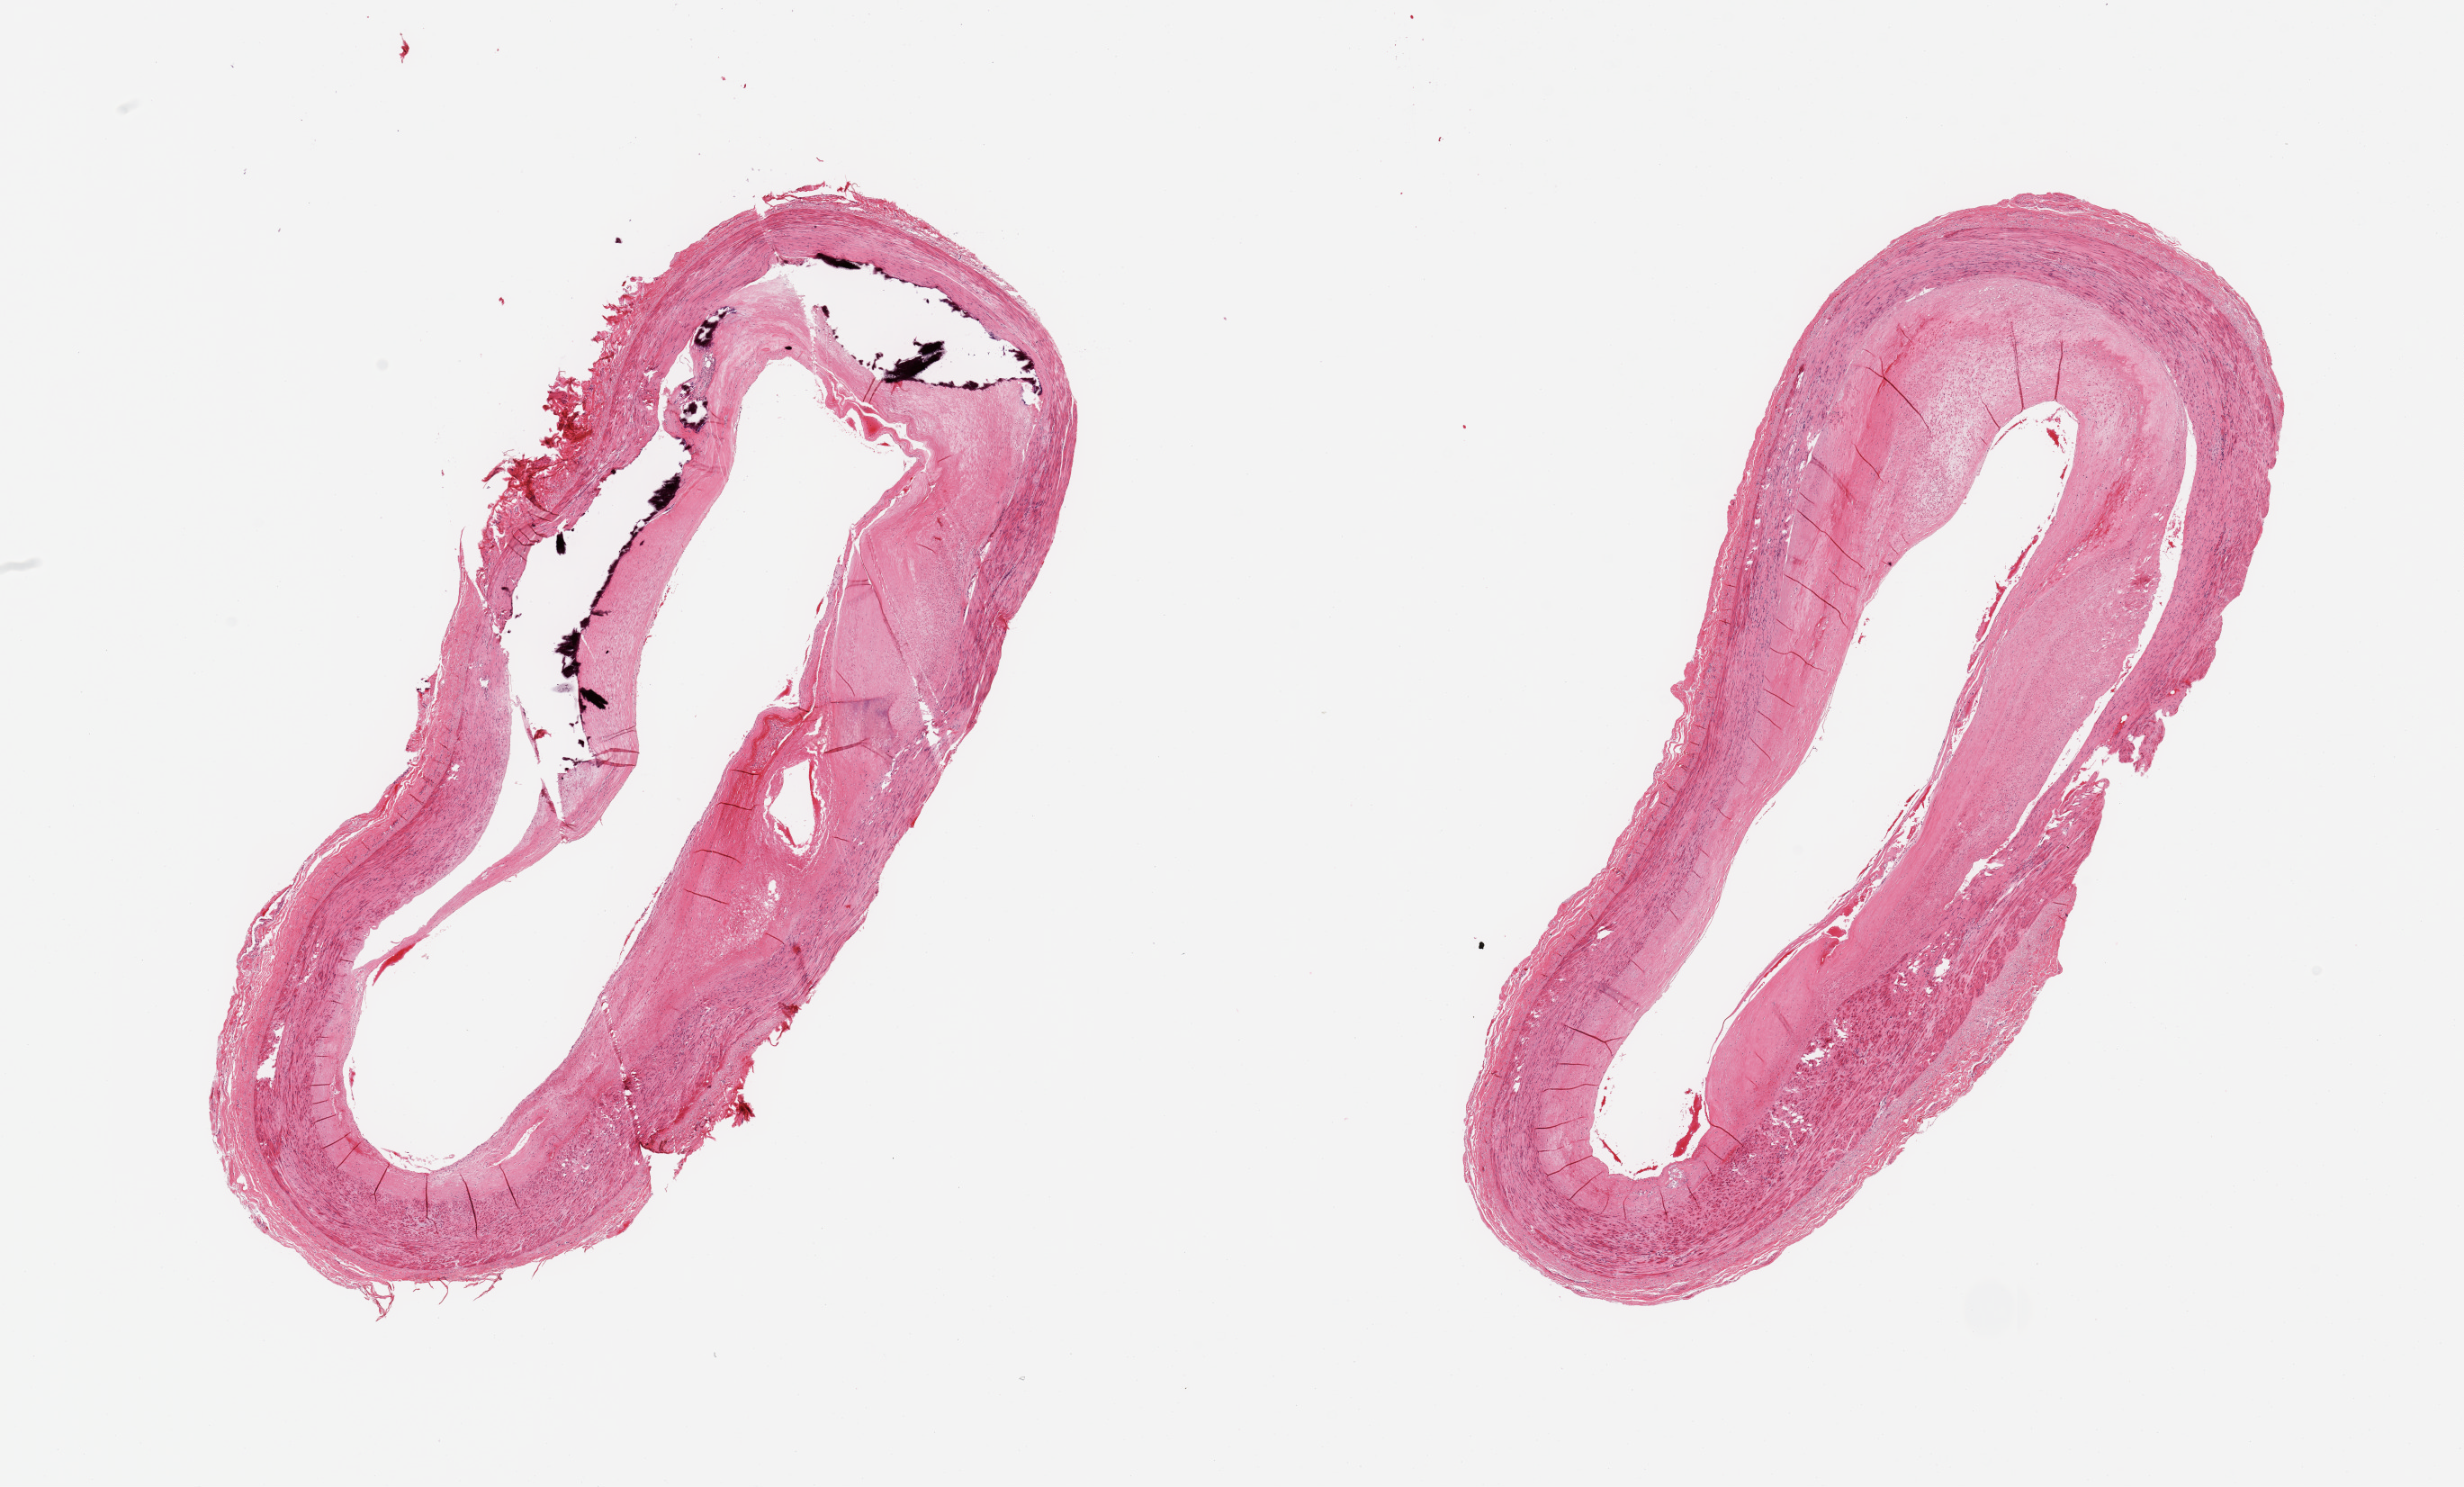
H&E whole-slide image, low-resolution overview of the scanned area, about 21.7 x 13.1 mm, PAXgene-fixed, paraffin-embedded tissue, target tissue: tibial artery, donor tissue sample. Male donor.
Reviewer comment on this tissue sample: 2 pieces, ~50-60% occlusive atherosis, focally calcified.